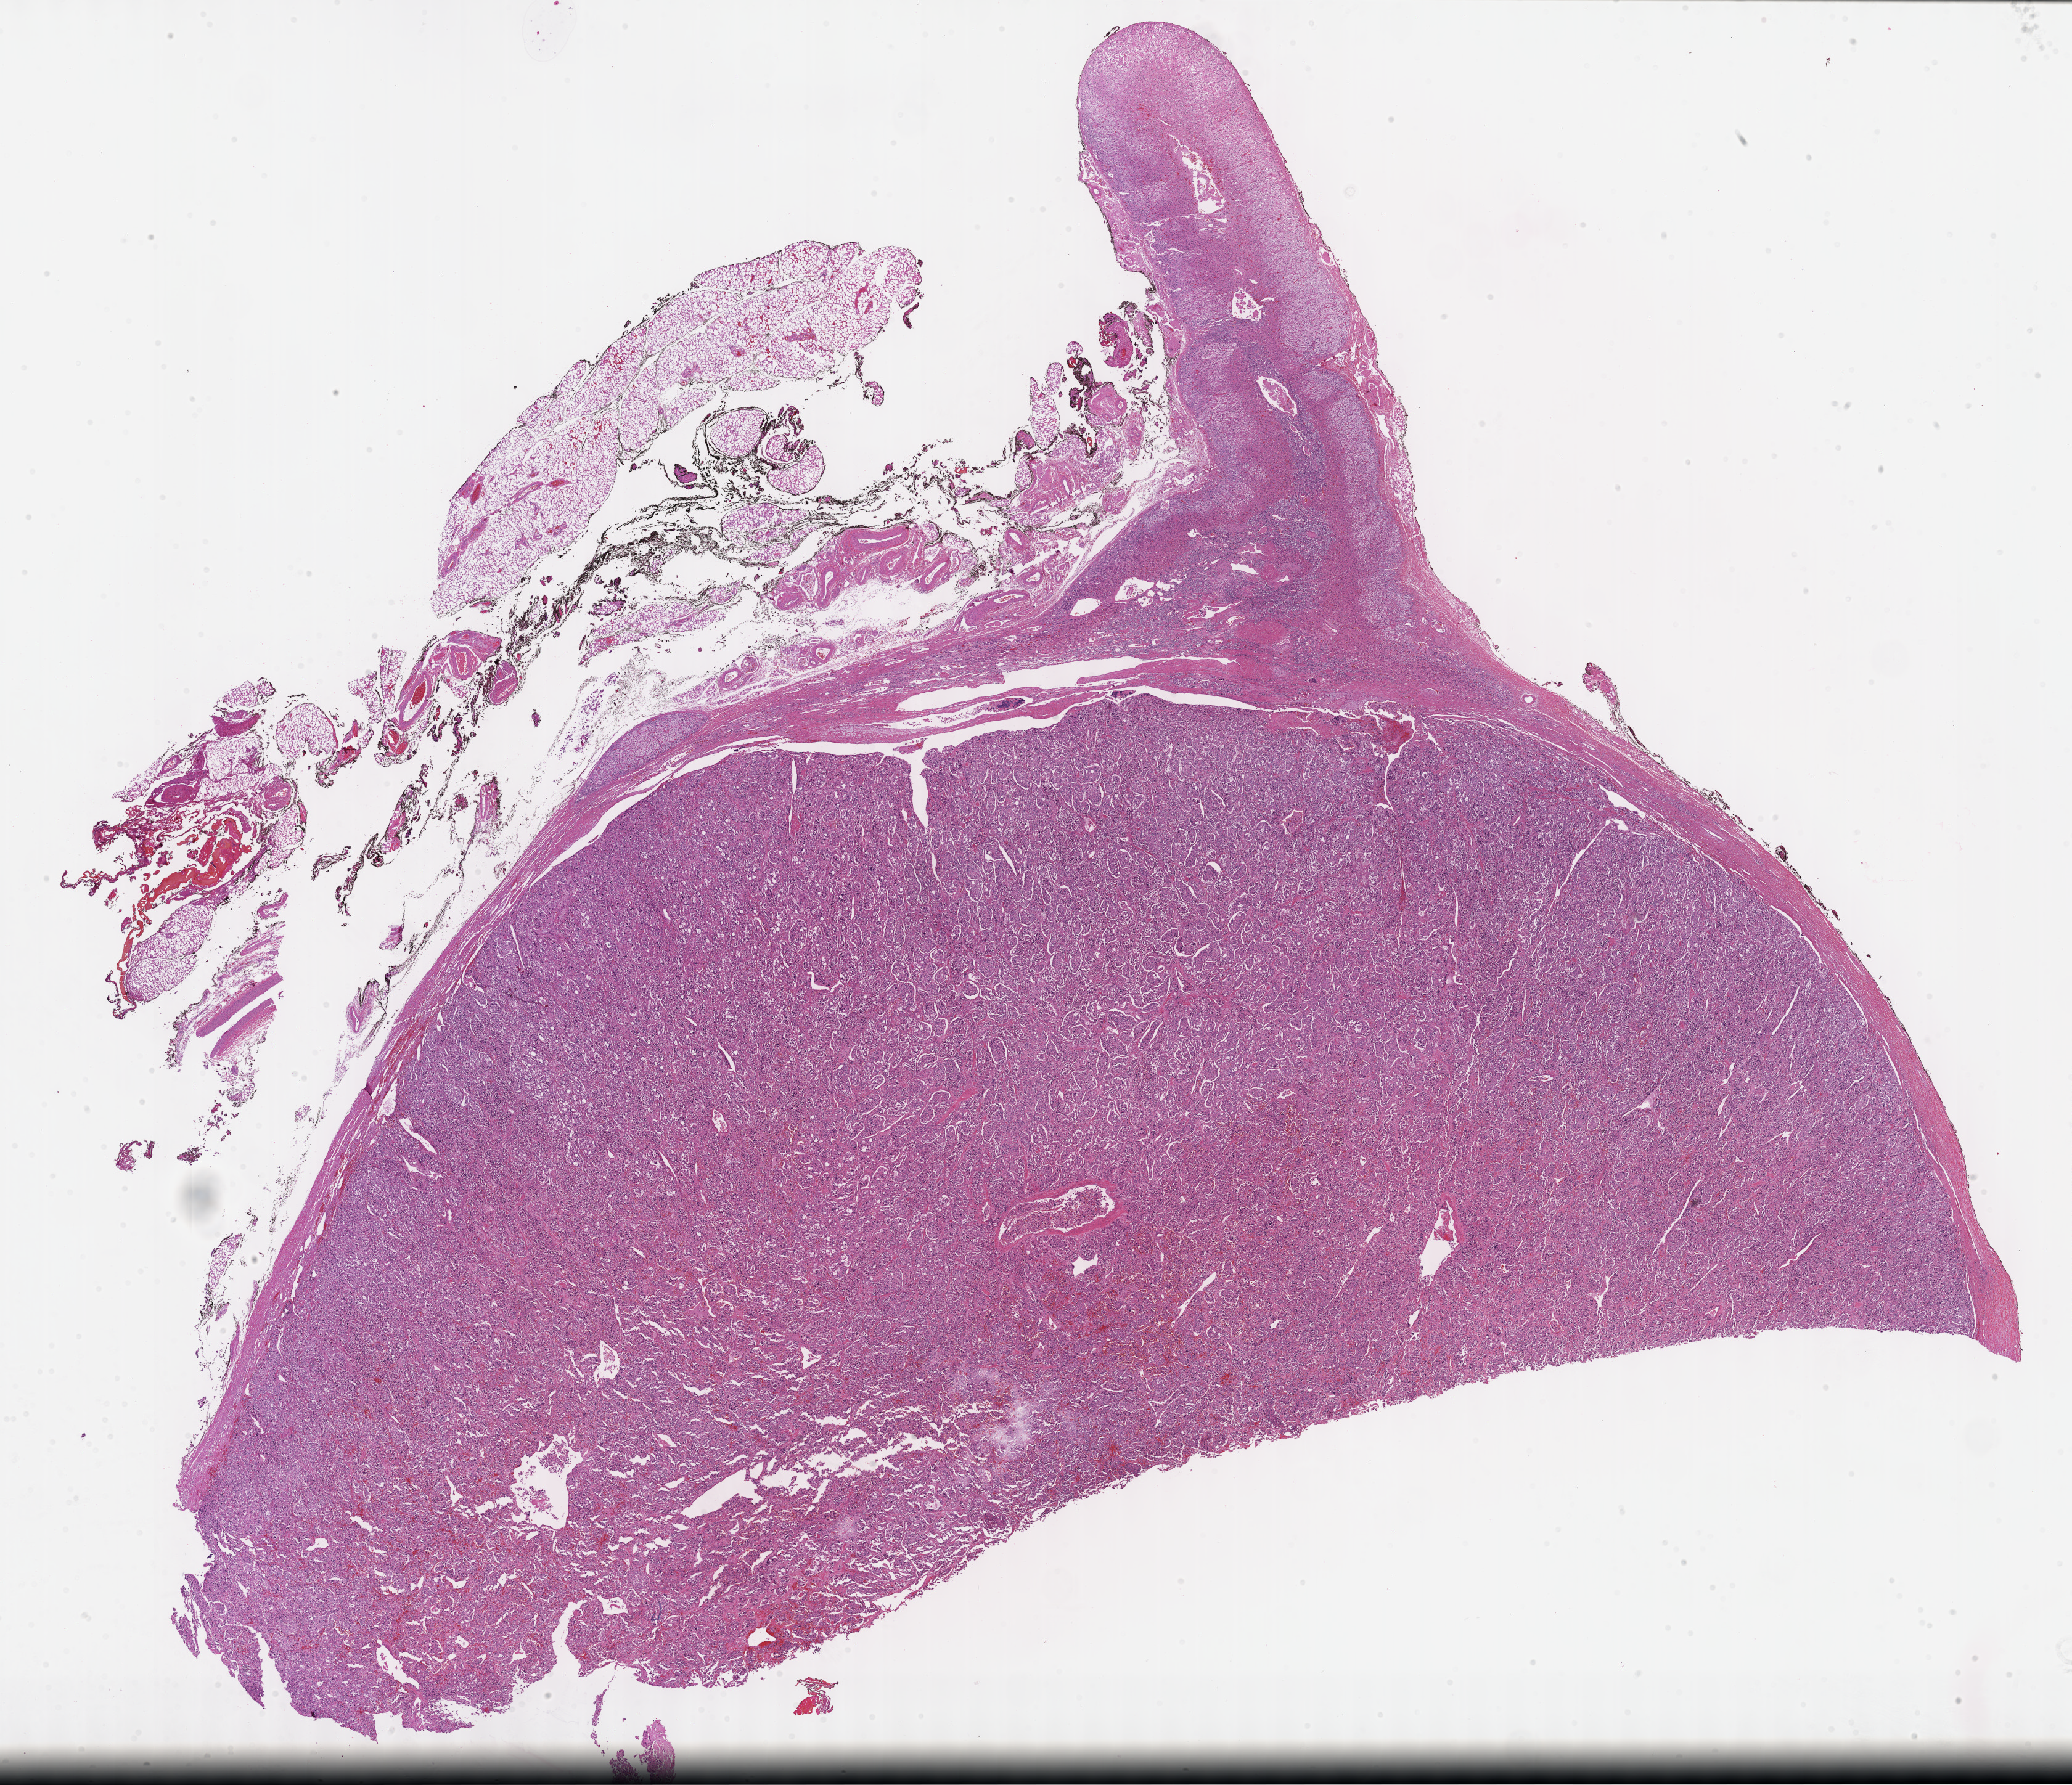
Whole-slide histology image, H&E-stained — shown as a low-resolution overview of the whole scanned area (about 27.2 x 23.4 mm, from a 40x scan), formalin-fixed paraffin-embedded (FFPE) diagnostic section, sample: primary tumour, adrenal gland. Female, age 28 years at initial diagnosis.
Histologic diagnosis: Pheochromocytoma, NOS.